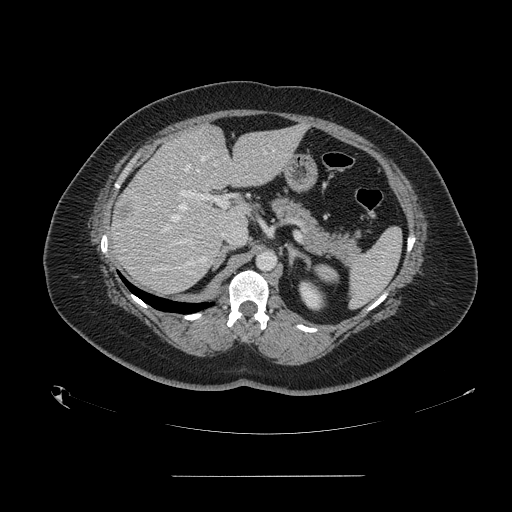
Contrast-enhanced abdominal CT, one axial slice. Position 94 of 164 along the scan axis. Intravenous contrast given. Soft-tissue window (W 400 / L 40 HU). 2.5 mm slice thickness. 512 × 512 image matrix, field of view 495 × 495 mm. Female patient, age 52 years. Case-level facts recorded for this patient, not image findings: diagnosis: colorectal cancer liver metastases, imaged before liver resection; multiple liver metastases: yes.
Outlined on this slice (expert manual segmentation):
- hepatic veins: bounding box <162,150,274,232> (left, top, right, bottom; pixels)
- liver: <111,126,303,293>
- planned liver remnant (the part of the liver to remain after resection): <175,125,302,227>
- portal vein (with intrahepatic branches): <177,190,228,243>
- liver metastasis: <118,204,131,221>